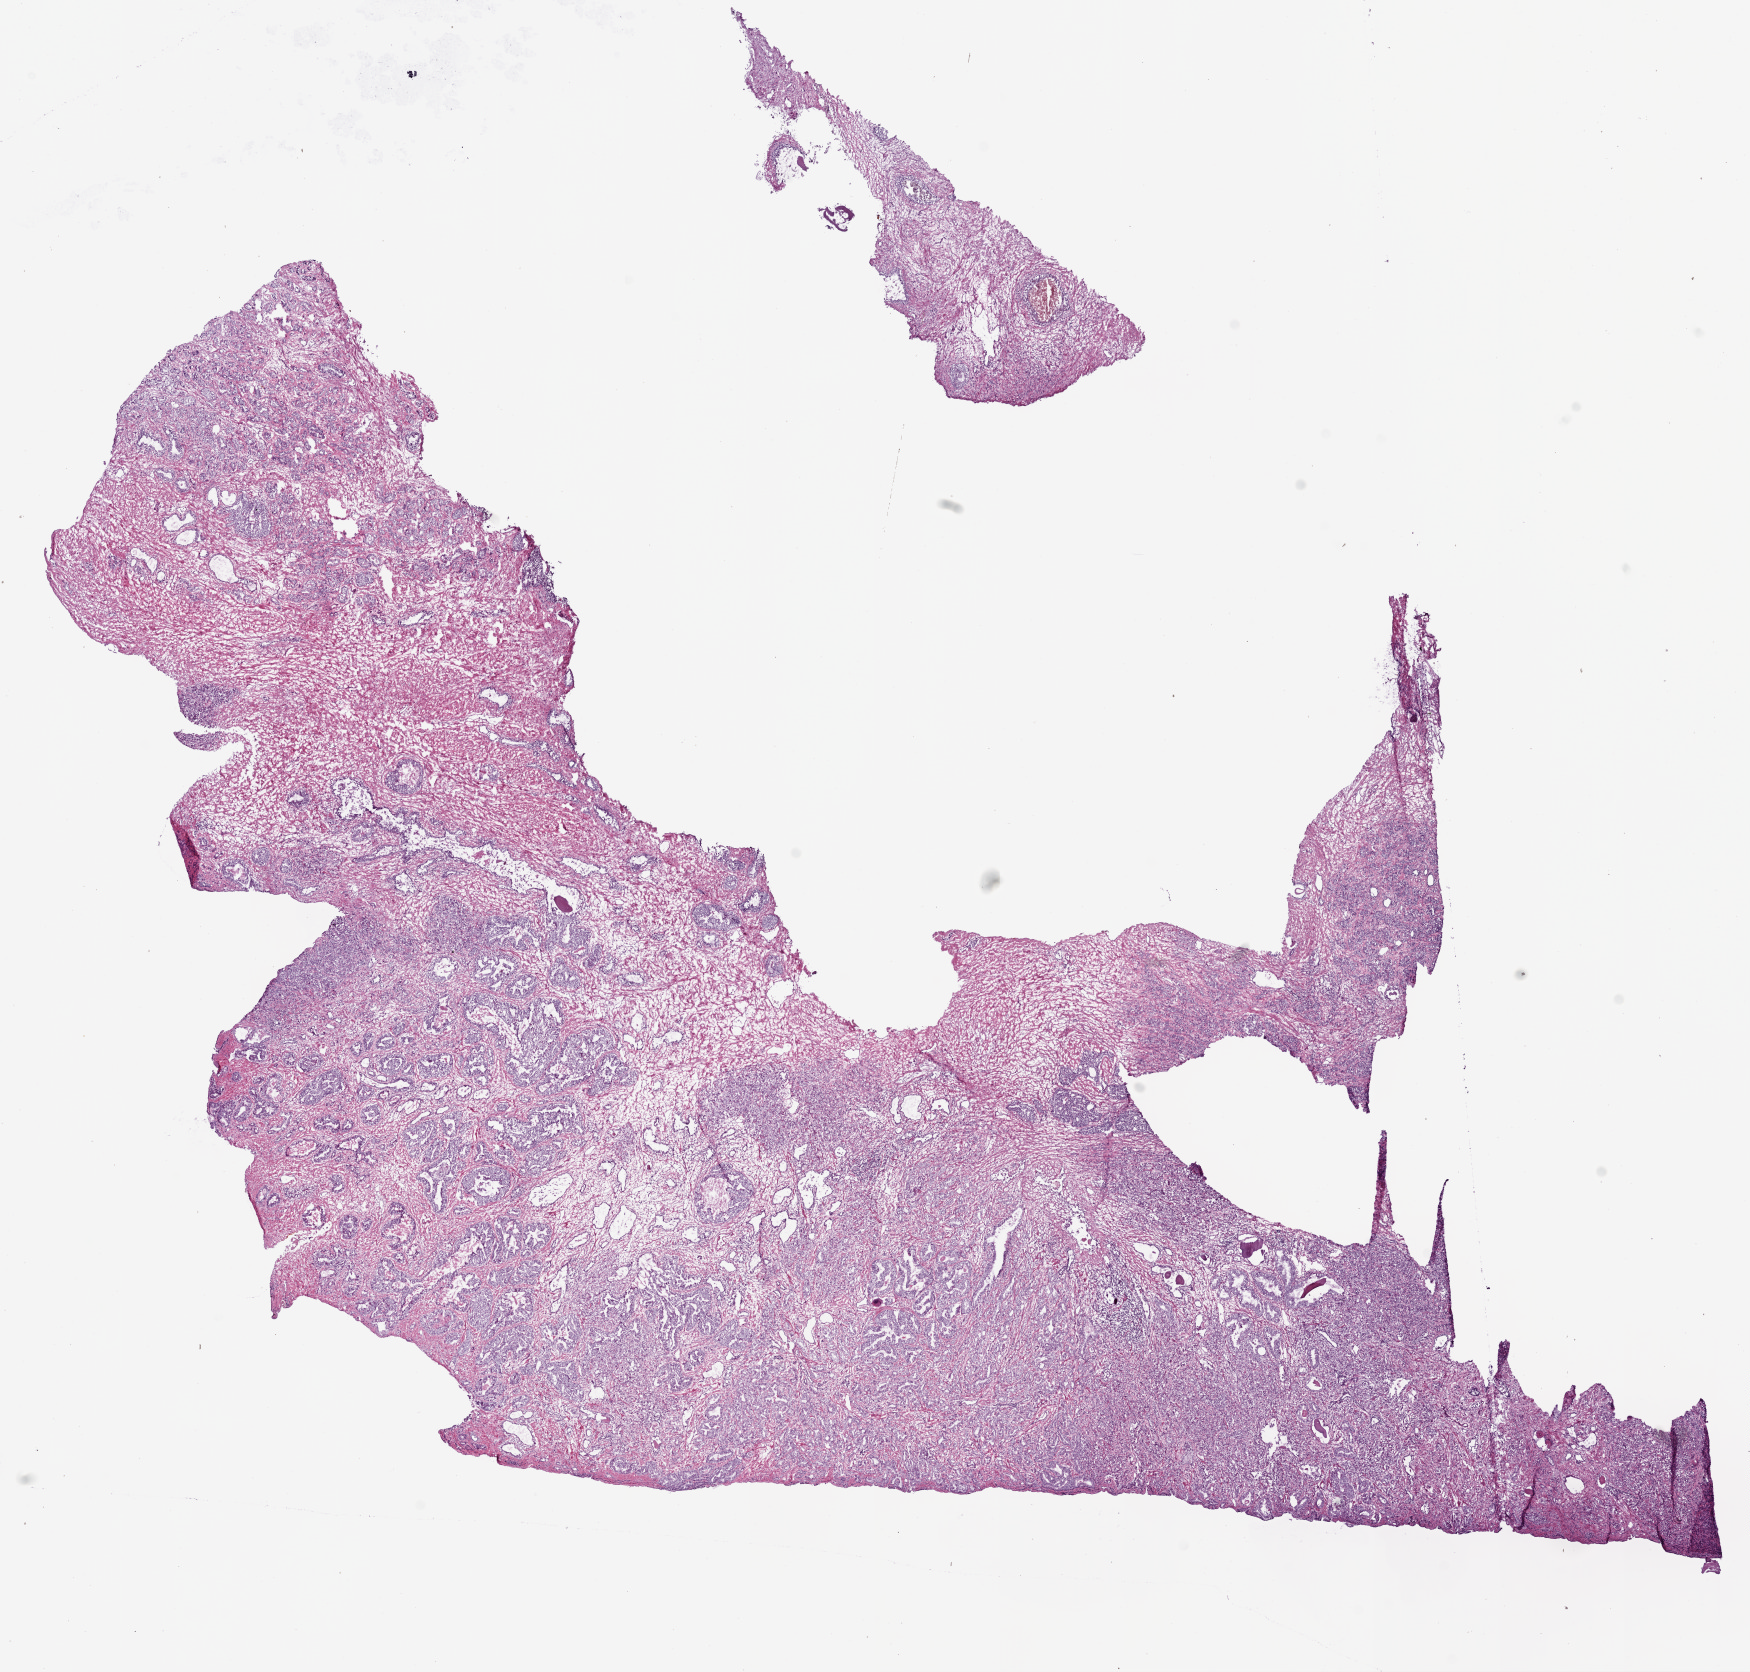
Hematoxylin and eosin (H&E) stained whole-slide image, whole scanned area (about 14.0 x 13.4 mm, from a 20x scan) shown as a low-resolution overview; frozen section from the bottom of the tissue portion; sample: primary tumour, prostate. Patient: male, age at initial diagnosis 68 years. Gleason score: 8 (5+3). Composition of this section per pathologist review: tumour cells 65%, tumour nuclei 60%, normal cells 15%, stromal cells 20%, necrosis 0%. Infiltration values recorded for this section: lymphocyte infiltration 4%, monocyte infiltration 0%, neutrophil infiltration 0%.
* laterality: bilateral
* pathologic diagnosis: Acinar cell carcinoma (prostate gland)